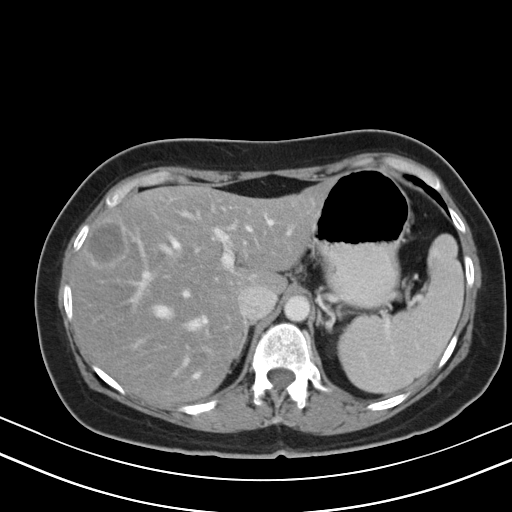
Contrast-enhanced abdominal CT, one axial slice. Position 34 of 47 along the scan axis. Soft-tissue window (W 400 / L 40 HU). 5 mm slice thickness. 512 × 512 image matrix. Female patient. Case-level facts recorded for this patient, not image findings: diagnosis: colorectal cancer liver metastases, imaged before liver resection; multiple liver metastases: no; largest metastasis: 3.5 cm; chemotherapy before resection: yes.
Annotated regions visible in this slice (outlined manually by an expert reader):
- hepatic veins: box from (x=156, y=215) to (x=290, y=377) px
- liver: (x=72, y=187)–(x=324, y=402)
- planned liver remnant (the part of the liver to remain after resection): (x=72, y=187)–(x=324, y=402)
- portal vein (with intrahepatic branches): (x=141, y=211)–(x=236, y=298)
- liver metastasis: (x=88, y=222)–(x=124, y=265)